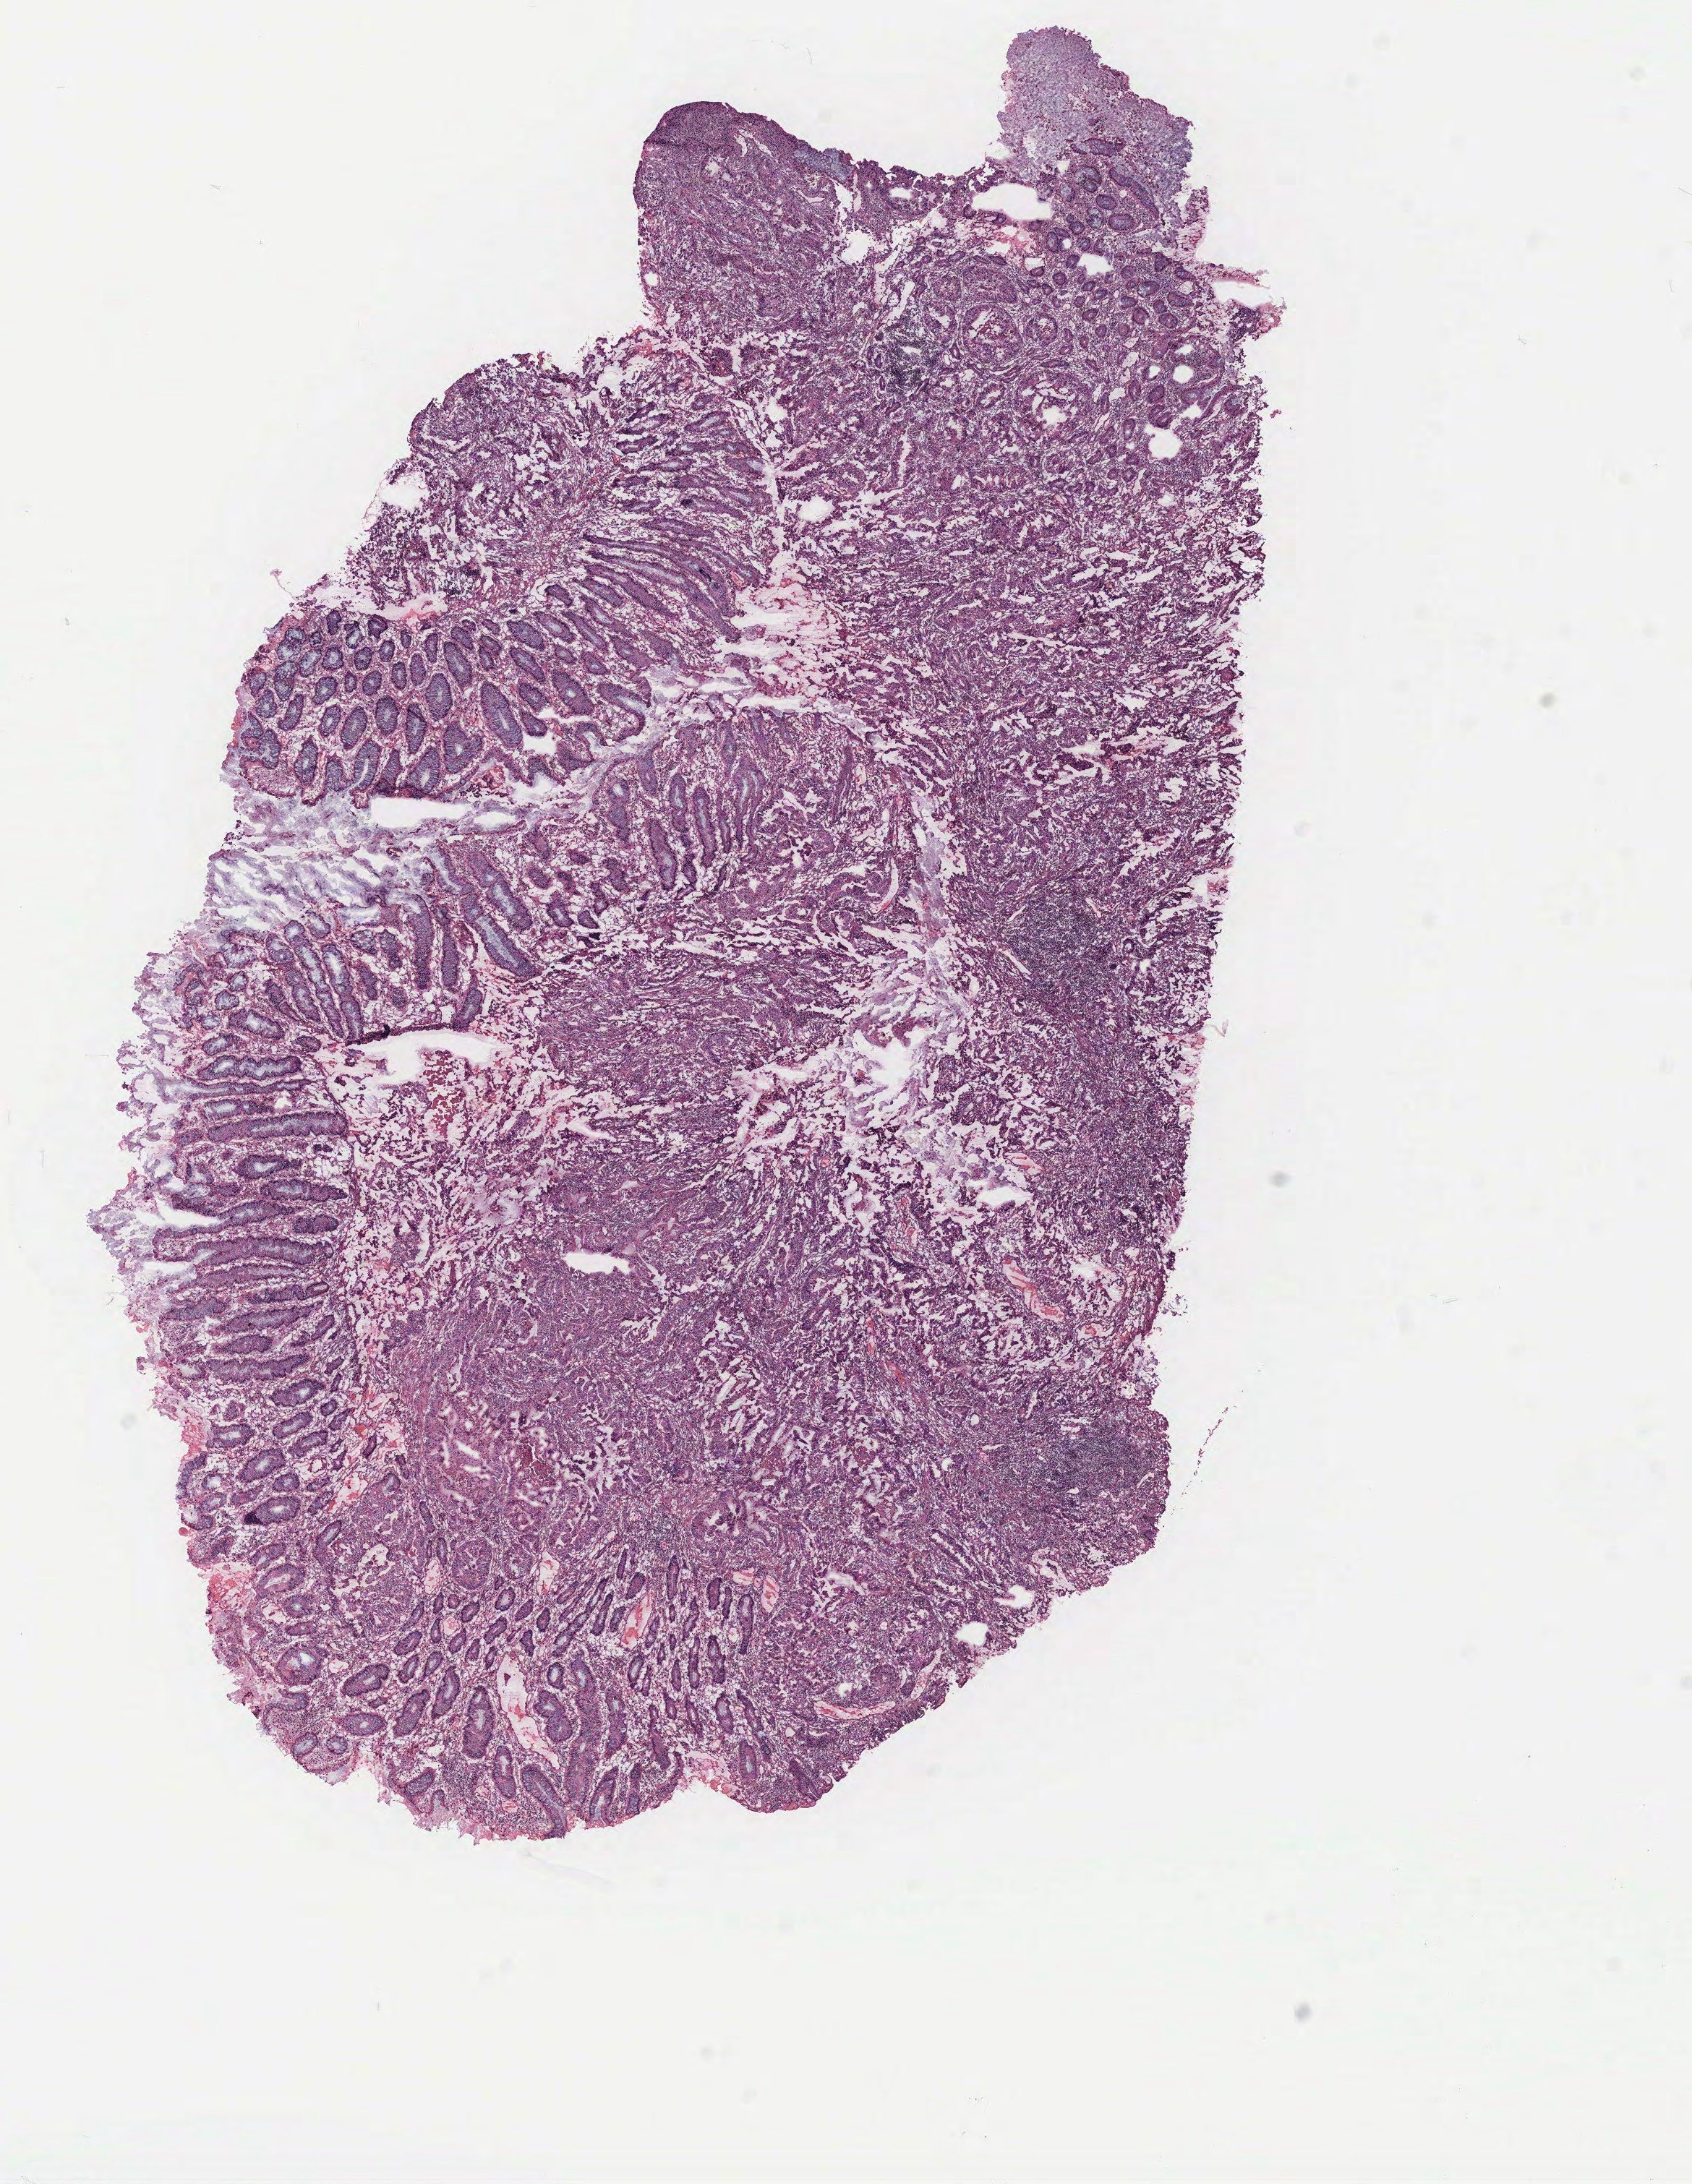
Hematoxylin and eosin (H&E) stained whole-slide image — a low-resolution overview of the entire scanned area, about 9.4 x 12.1 mm (from a 40x scan); normal (non-tumour) tissue sample, colon. Male, 60 y/o.
This section: normal (non-tumour) tissue from the same patient. Patient diagnosis: Adenocarcinoma, NOS.